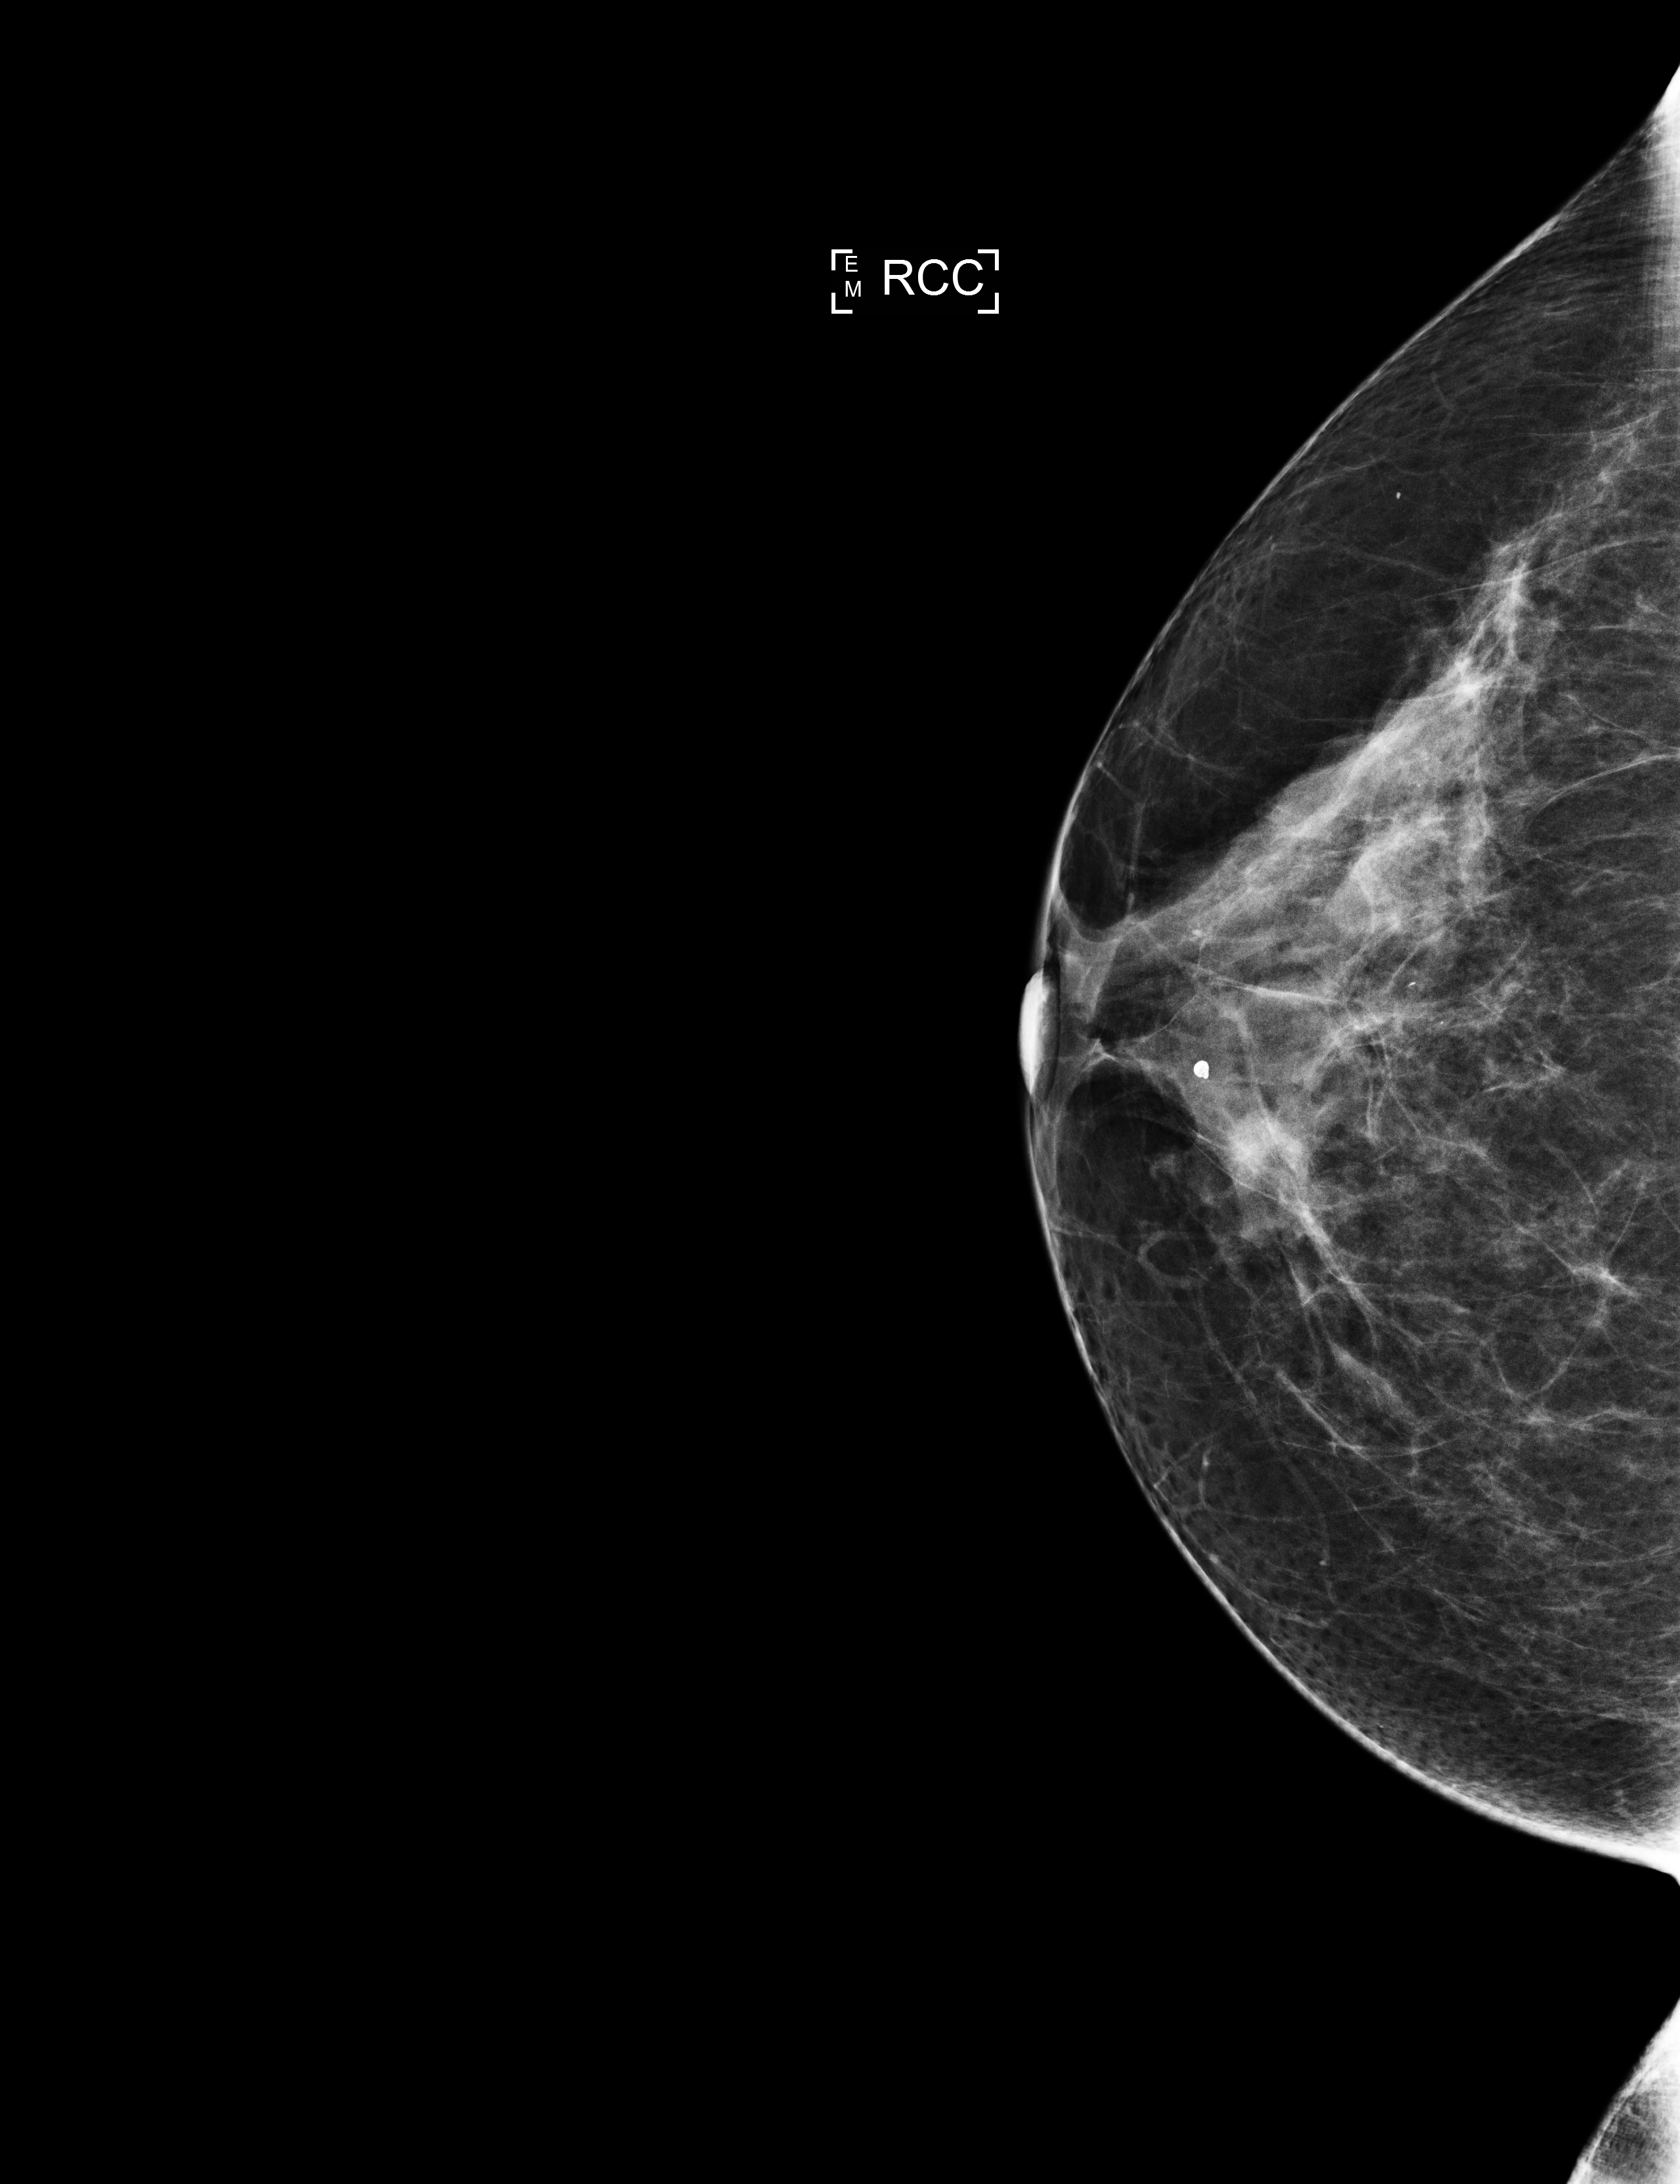
Annual screening mammography examination; compressed breast thickness 59 mm. Female patient, age 57 years.
Image type: full-field digital mammogram. Breast: right. Projection: cranio-caudal projection.